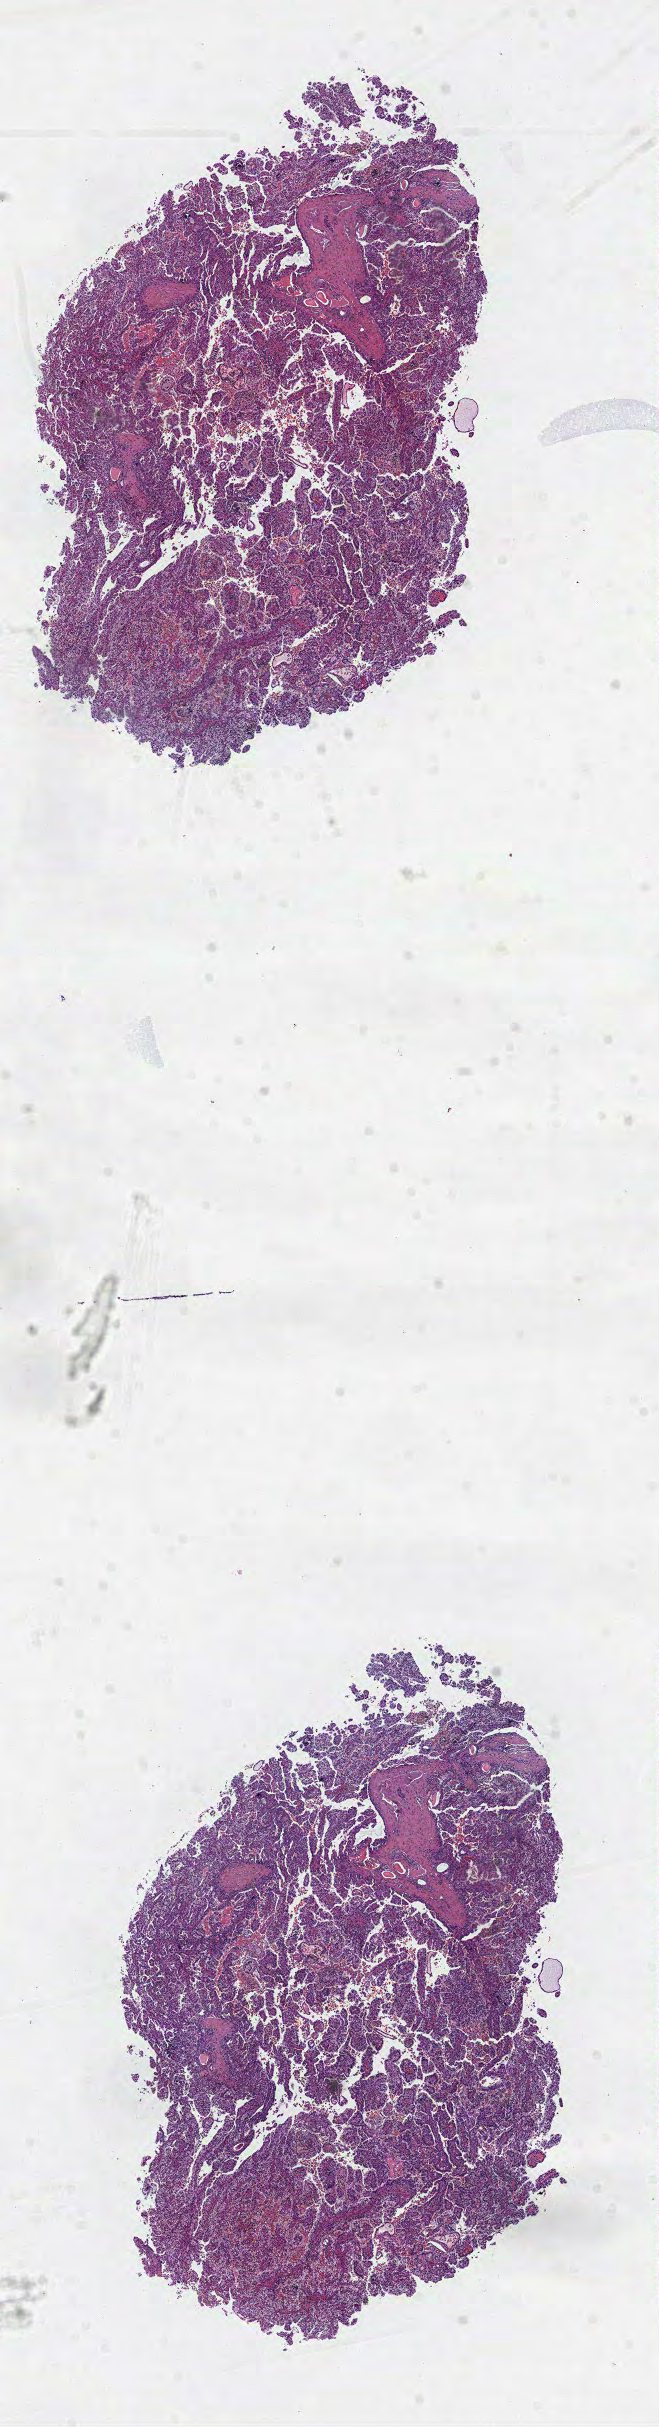
H&E-stained whole-slide image, whole scanned area (about 5.3 x 19.6 mm, from a 40x scan) shown as a low-resolution overview. Formalin-fixed paraffin-embedded (FFPE) diagnostic section. Primary tumour sample from the kidney. Male, age 52 years at initial diagnosis.
- AJCC pathologic stage: III
- pathologic diagnosis: Papillary adenocarcinoma, NOS